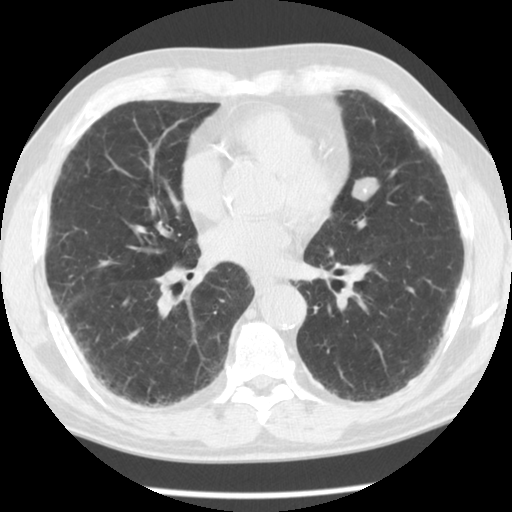
Low-dose screening chest CT, one axial slice; slice 52 of 113 in the series (ordered by position); reconstruction kernel STANDARD; 120 kVp; lung window (W 1500 / L -600 HU); 2.5 mm slice thickness; 512 × 512 image matrix.
Structures marked on this image (outlined manually by an expert reader):
- lesion 1 (nodule, upper lobe of left lung): bounding box (x1, y1, x2, y2) in pixels: (352, 177, 379, 201)